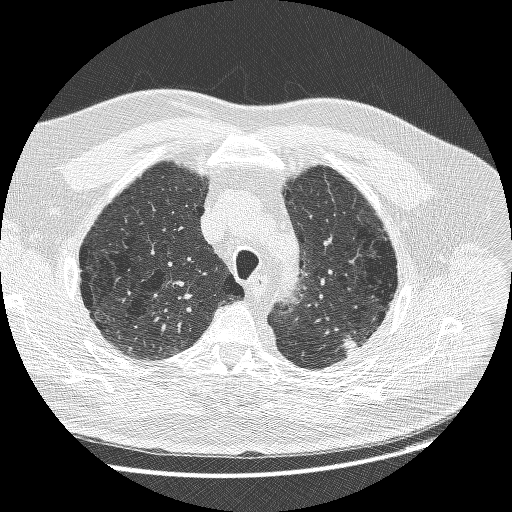
Axial slice from a low-dose chest CT screening exam. First (baseline) screen. Lung window (W 1500 / L -600 HU). 1.25 mm slice thickness. Lung (sharp) reconstruction kernel (BONE). Slice 207 of 258 in the series. 512 × 512 image matrix, field of view 370 × 370 mm. Male participant, aged 68 years at enrolment. Former smoker at enrolment.
Lesion marked by an expert reader, box from (x=329, y=324) to (x=388, y=366) px. The exam's reader record, not a measurement of the box and not confirmed to be the same lesion: non-calcified nodule or mass ≥4 mm, left upper lobe, 15 × 14 mm, smooth margins, soft tissue attenuation. Official screen result: positive, change unspecified: nodule(s) >= 4 mm or enlarging nodule(s), mass(es), or other non-specific abnormalities suspicious for lung cancer. Participant outcome: lung cancer diagnosed 19 days after this screen — adenosquamous carcinoma, left upper lobe, poorly differentiated (G3), stage IIIB (AJCC 6th edition), 32 mm at pathology.